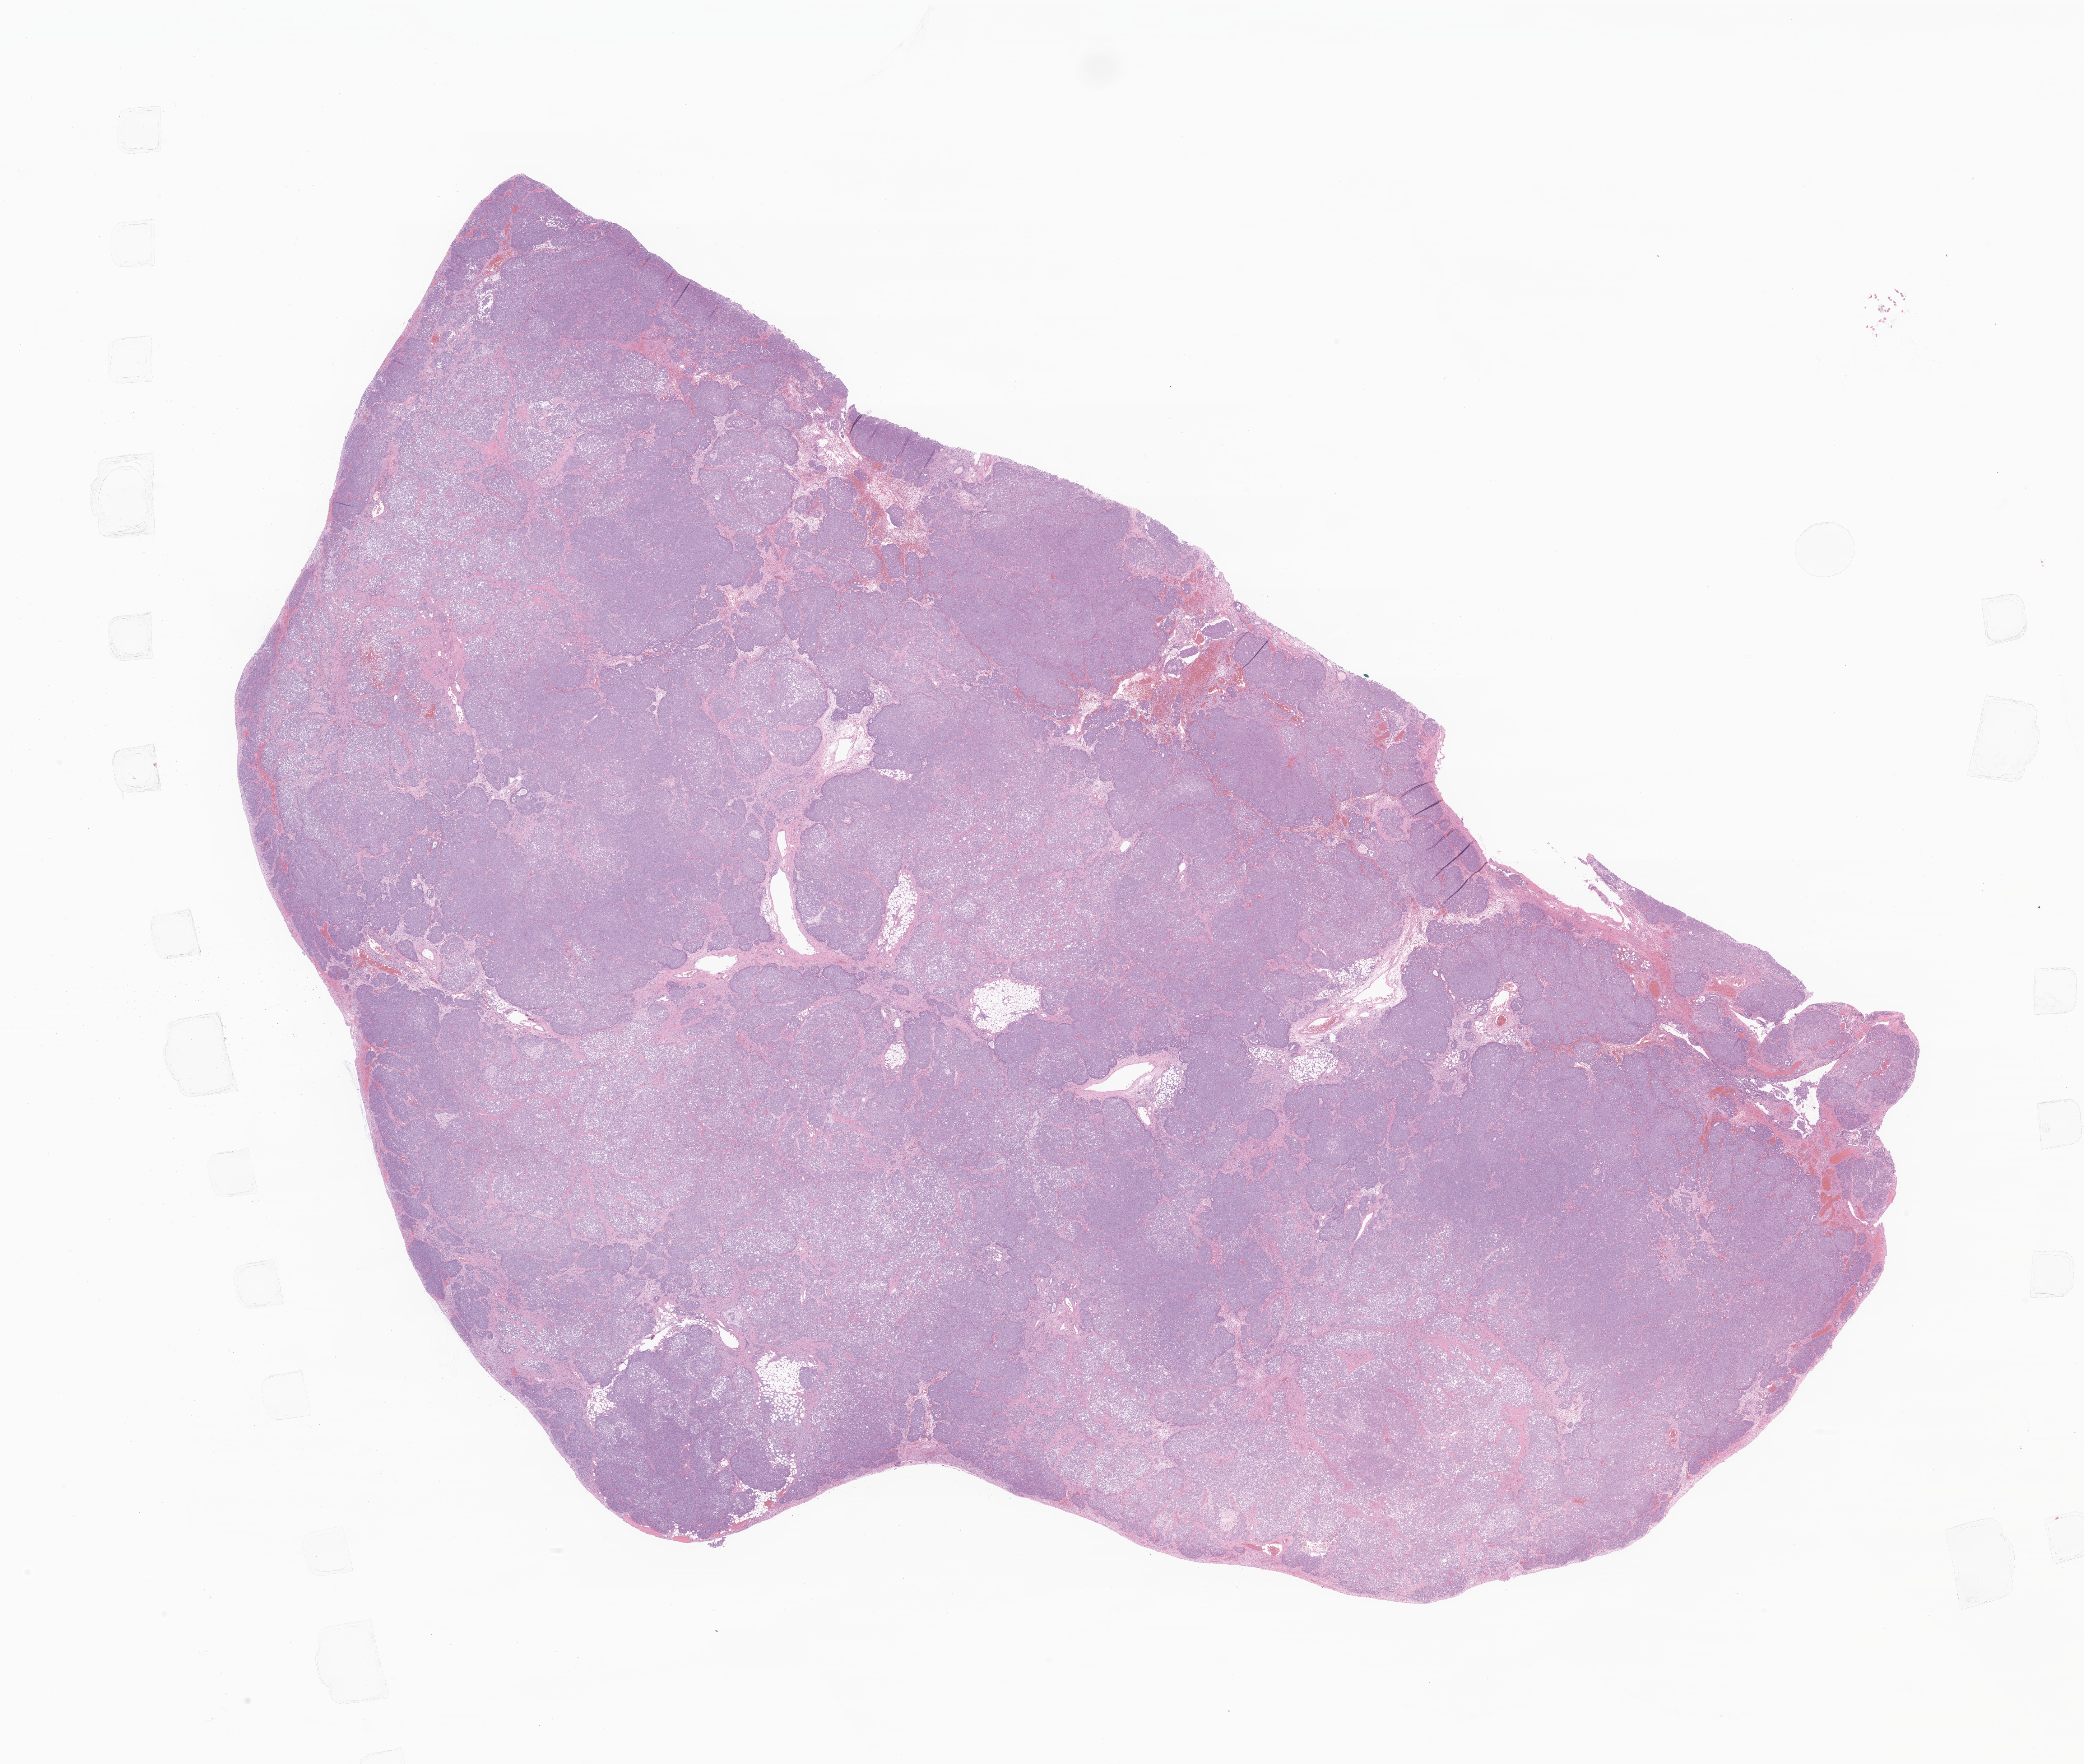
Digitized H&E-stained section of tumor tissue from the pancreatic duct — whole scanned area (about 24.5 x 20.7 mm) shown as a low-resolution overview, formalin-fixed, paraffin-embedded (FFPE) tissue. Patient female; age 56 months (4 years 8 months).
Diagnosis (ICD-O-3 morphology term): Acinar cell carcinoma.